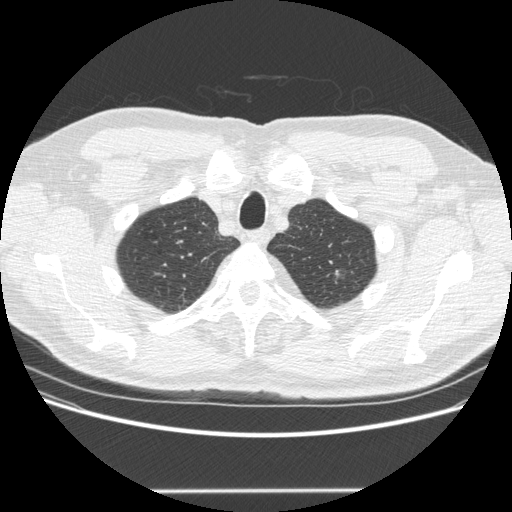
Chest CT (low-dose screening protocol), one axial image. Second screening round (one year after baseline). Lung window (W 1500 / L -600 HU). 1.25 mm slice thickness. Standard (soft-tissue) reconstruction kernel (STANDARD). Slice 49 of 223 in the series. Male, age 69 years at enrolment.
- Expert reader's lesion annotation, bounding box [x1, y1, x2, y2] px = [311, 261, 347, 293].
- No non-calcified nodule or mass ≥4 mm was recorded by the screening reader at this exam.